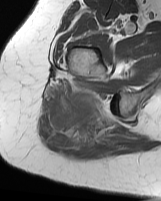
MRI of an extremity soft-tissue mass, one axial slice. Slice 45 of 70 in the series (ordered by position). MR volume resampled by the dataset authors to the PET/CT grid (not the native acquisition matrix). 3.27 mm slice thickness. 161 × 201 image matrix, field of view 157 × 196 mm. Female patient. From the clinical record (not read from this slice): histological type: synovial sarcoma; grade: intermediate; site of the primary tumour: right buttock.
Outlined on this slice (expert contour drawn on MRI and transferred to this co-registered scan by the dataset authors):
- gross tumour volume including surrounding oedema: bounding box [x1, y1, x2, y2] px = [53, 90, 125, 151]
- gross tumour volume (mass): [53, 90, 100, 125]